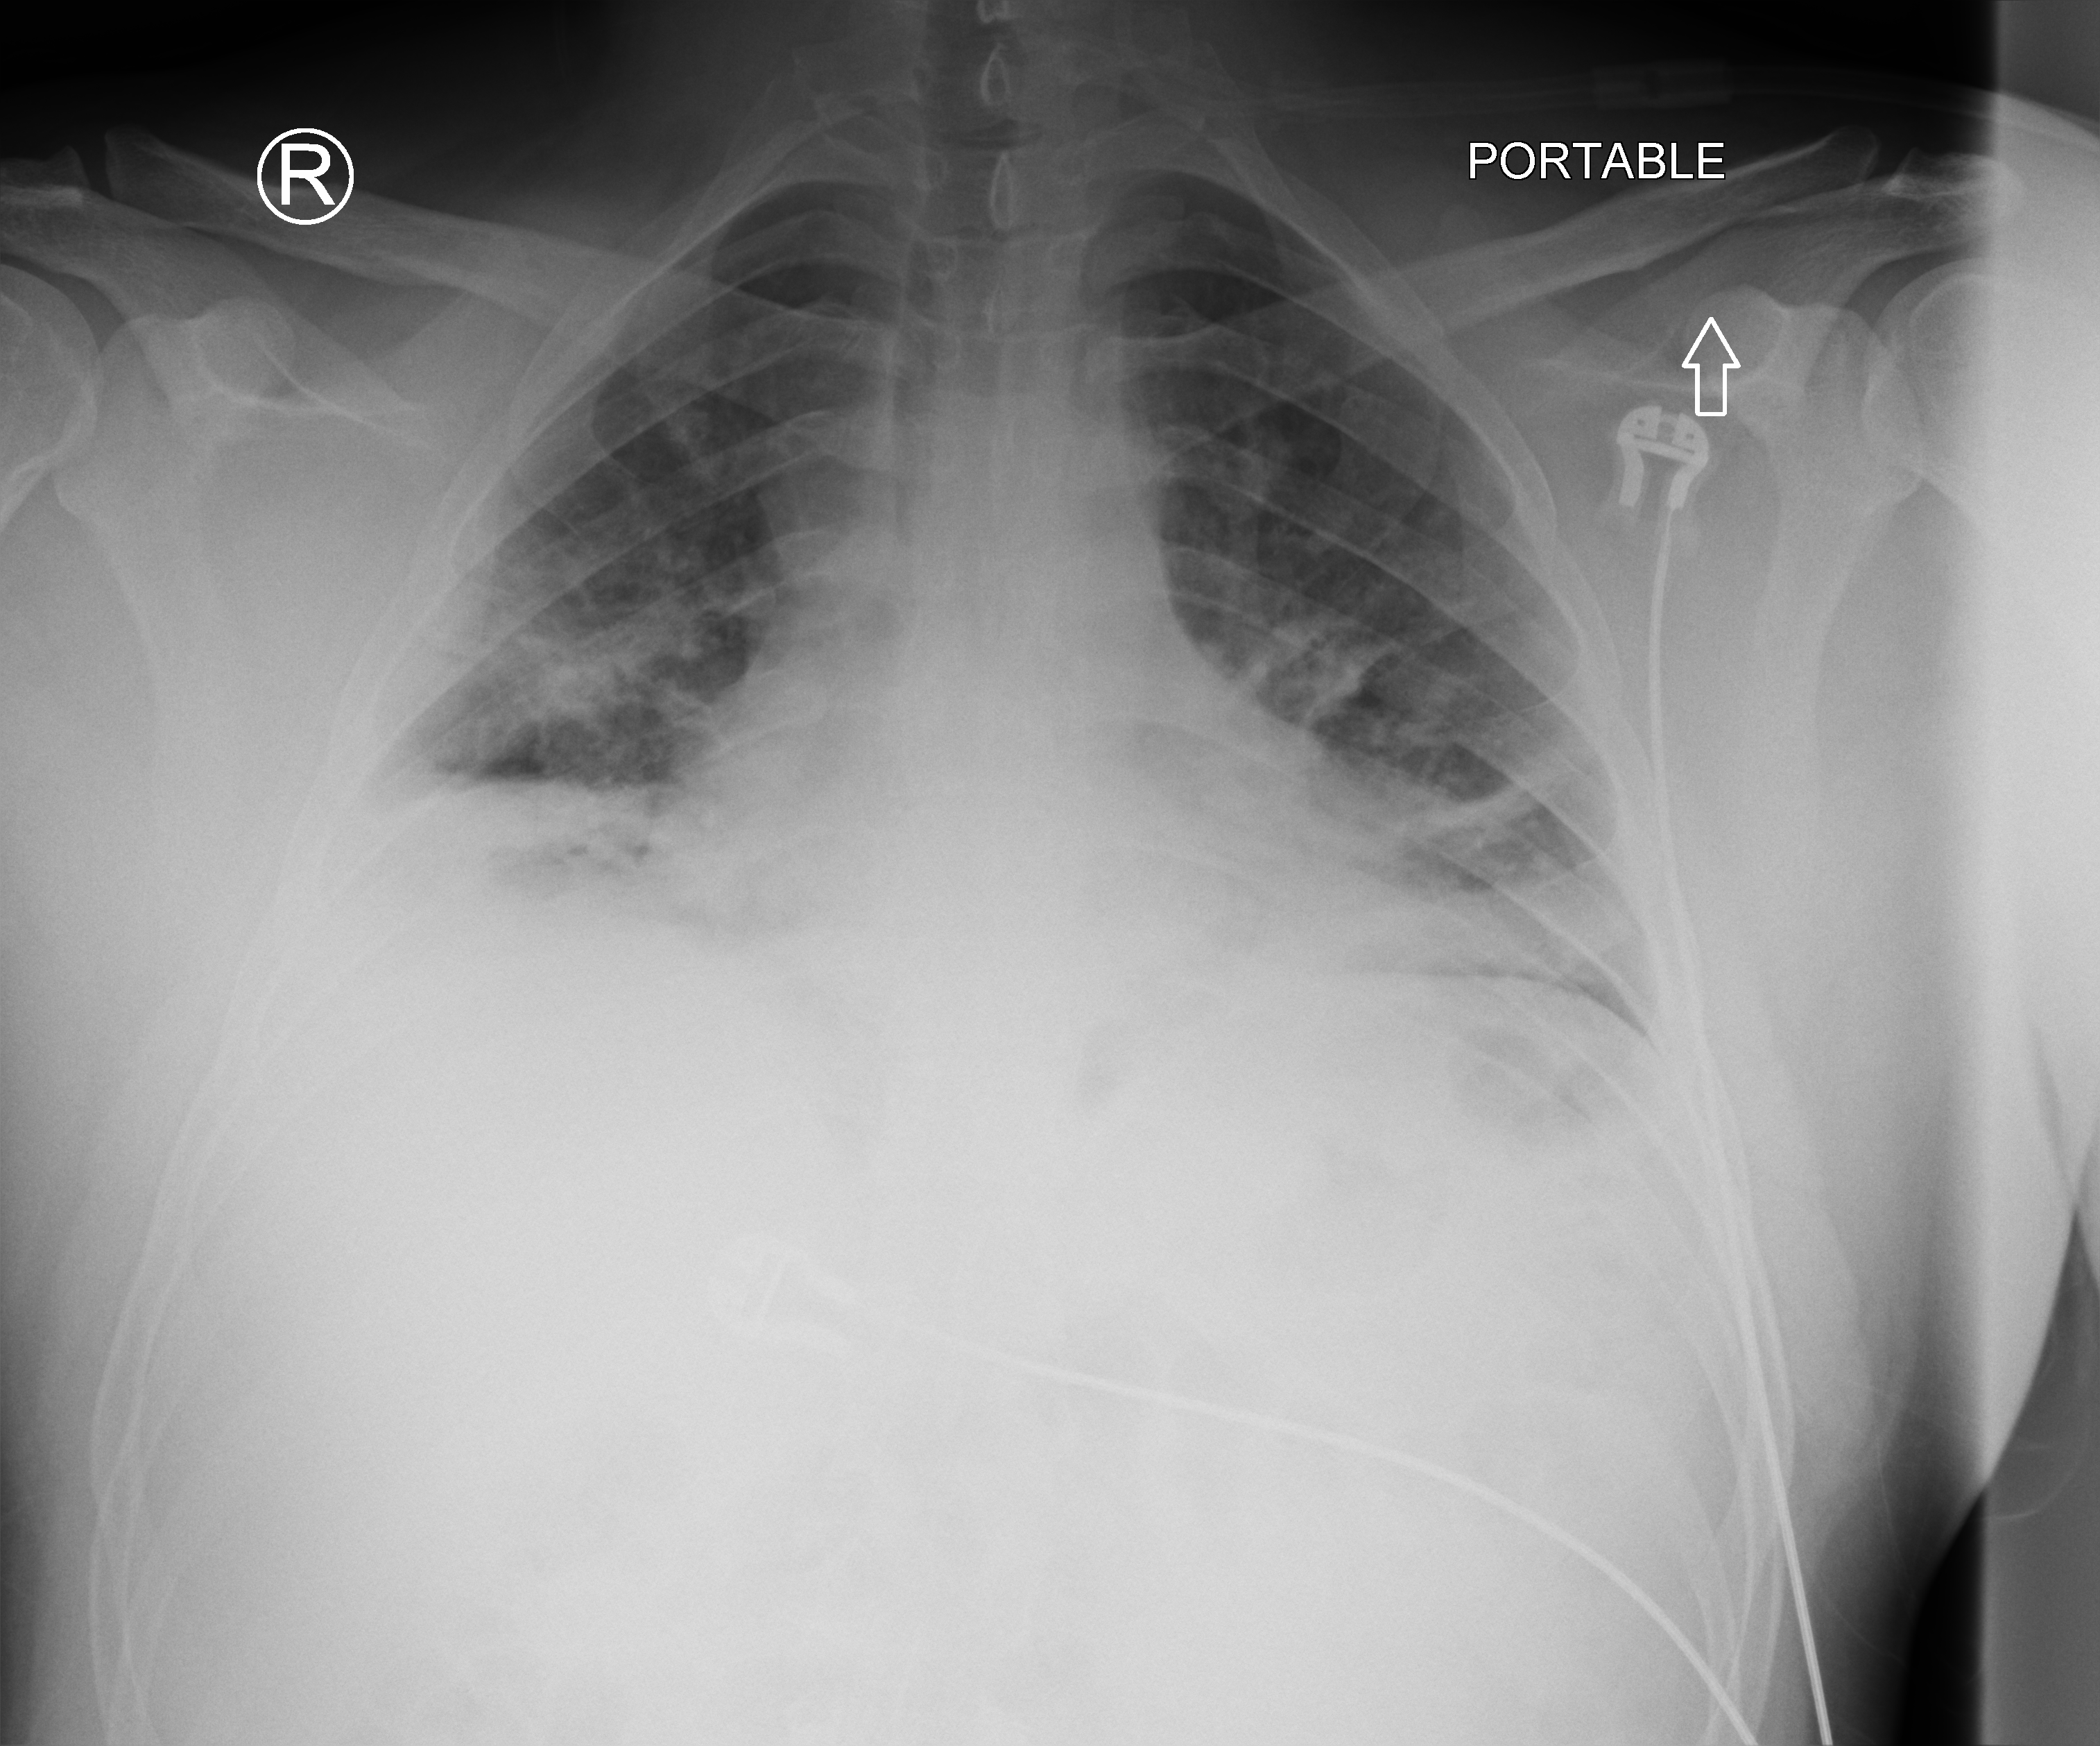
Bedside chest radiograph (computed radiography); anteroposterior (AP) projection. Male patient hospitalised with COVID-19, age 18–59 years.
Admission-level facts for this patient (not findings on this image; timing relative to this image not recorded): mechanically ventilated during this hospital stay: no; COPD (admission record): no.